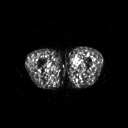
FDG PET of an extremity soft-tissue mass (from a PET/CT study), one axial slice. Position 230 of 311 along the scan axis. 3.27 mm slice thickness. 128 × 128 image matrix, field of view 500 × 500 mm. Patient: male, 29 years. Case-level facts recorded for this patient, not image findings: histological type: mixoid liposarcoma; grade: low; site of the primary tumour: left thigh.
Annotated regions visible in this slice (expert contour drawn on MRI and transferred to this co-registered scan by the dataset authors):
- gross tumour volume (mass): bounding box [x1, y1, x2, y2] px = [72, 56, 81, 67]